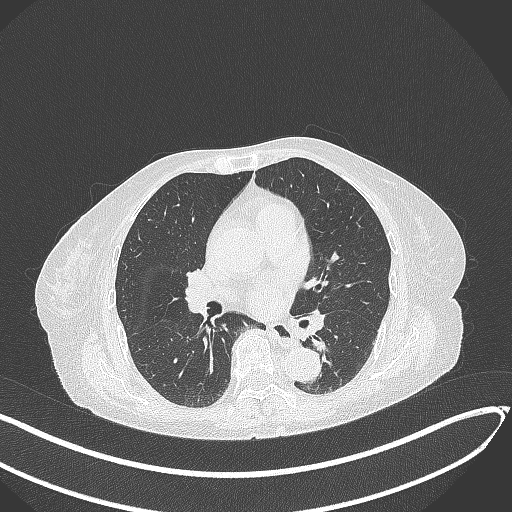
Chest CT, one axial slice; position 133 of 324 along the scan axis; 120 kVp; lung window (W 1500 / L -600 HU); 512 × 512 image matrix. Female patient, age 82 years. Case-level facts recorded for this patient, not image findings: clinical TNM (as recorded): T1b N0 M1.
Outlined on this slice (bounding box drawn by a radiologist):
- lung tumour (recorded histology: adenocarcinoma): bounding box [x1, y1, x2, y2] px = [312, 336, 331, 355]